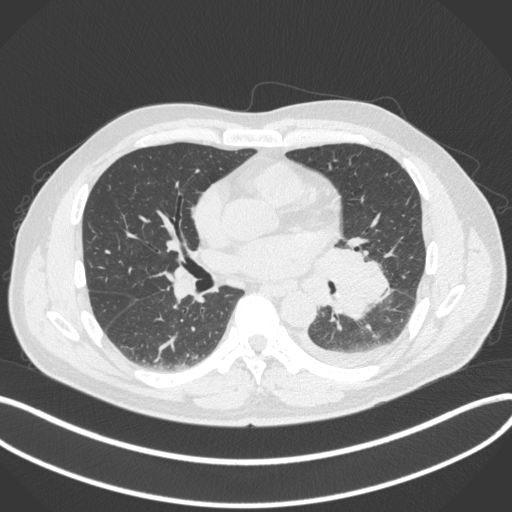
Chest CT, one axial slice; slice 180 of 350 in the series (ordered by position); 120 kVp; lung window (W 1500 / L -600 HU); 1 mm slice thickness; 512 × 512 image matrix, field of view 400 × 400 mm. Male patient, age 58 years. Case-level facts recorded for this patient, not image findings: clinical TNM (as recorded): T3 N1 M1b; histopathological grade: G3.
Structures marked on this image (rectangle marked by the reading radiologist):
- lung tumour (recorded histology: small cell carcinoma): bounding box (x1, y1, x2, y2) in pixels: (315, 243, 393, 316)